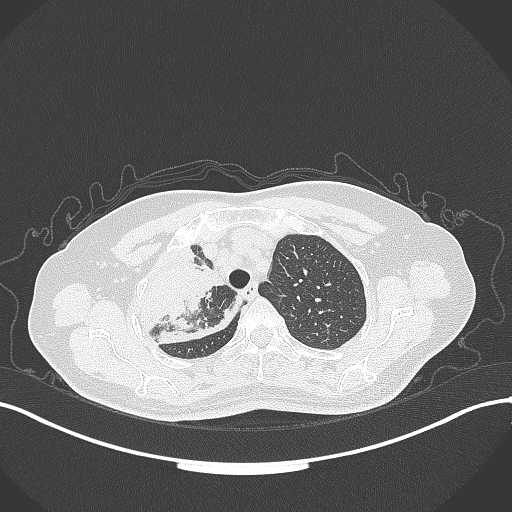
Chest CT, one axial slice; position 253 of 309 along the scan axis; reconstruction kernel B70f; 120 kVp; lung window (W 1500 / L -600 HU); 1 mm slice thickness; 512 × 512 image matrix, field of view 400 × 400 mm. Female patient, age 60 years. Case-level facts recorded for this patient, not image findings: clinical TNM (as recorded): T3 N1 M1.
Structures marked on this image (rectangle marked by the reading radiologist):
- lung tumour (recorded histology: adenocarcinoma): box from (x=130, y=240) to (x=245, y=347) px